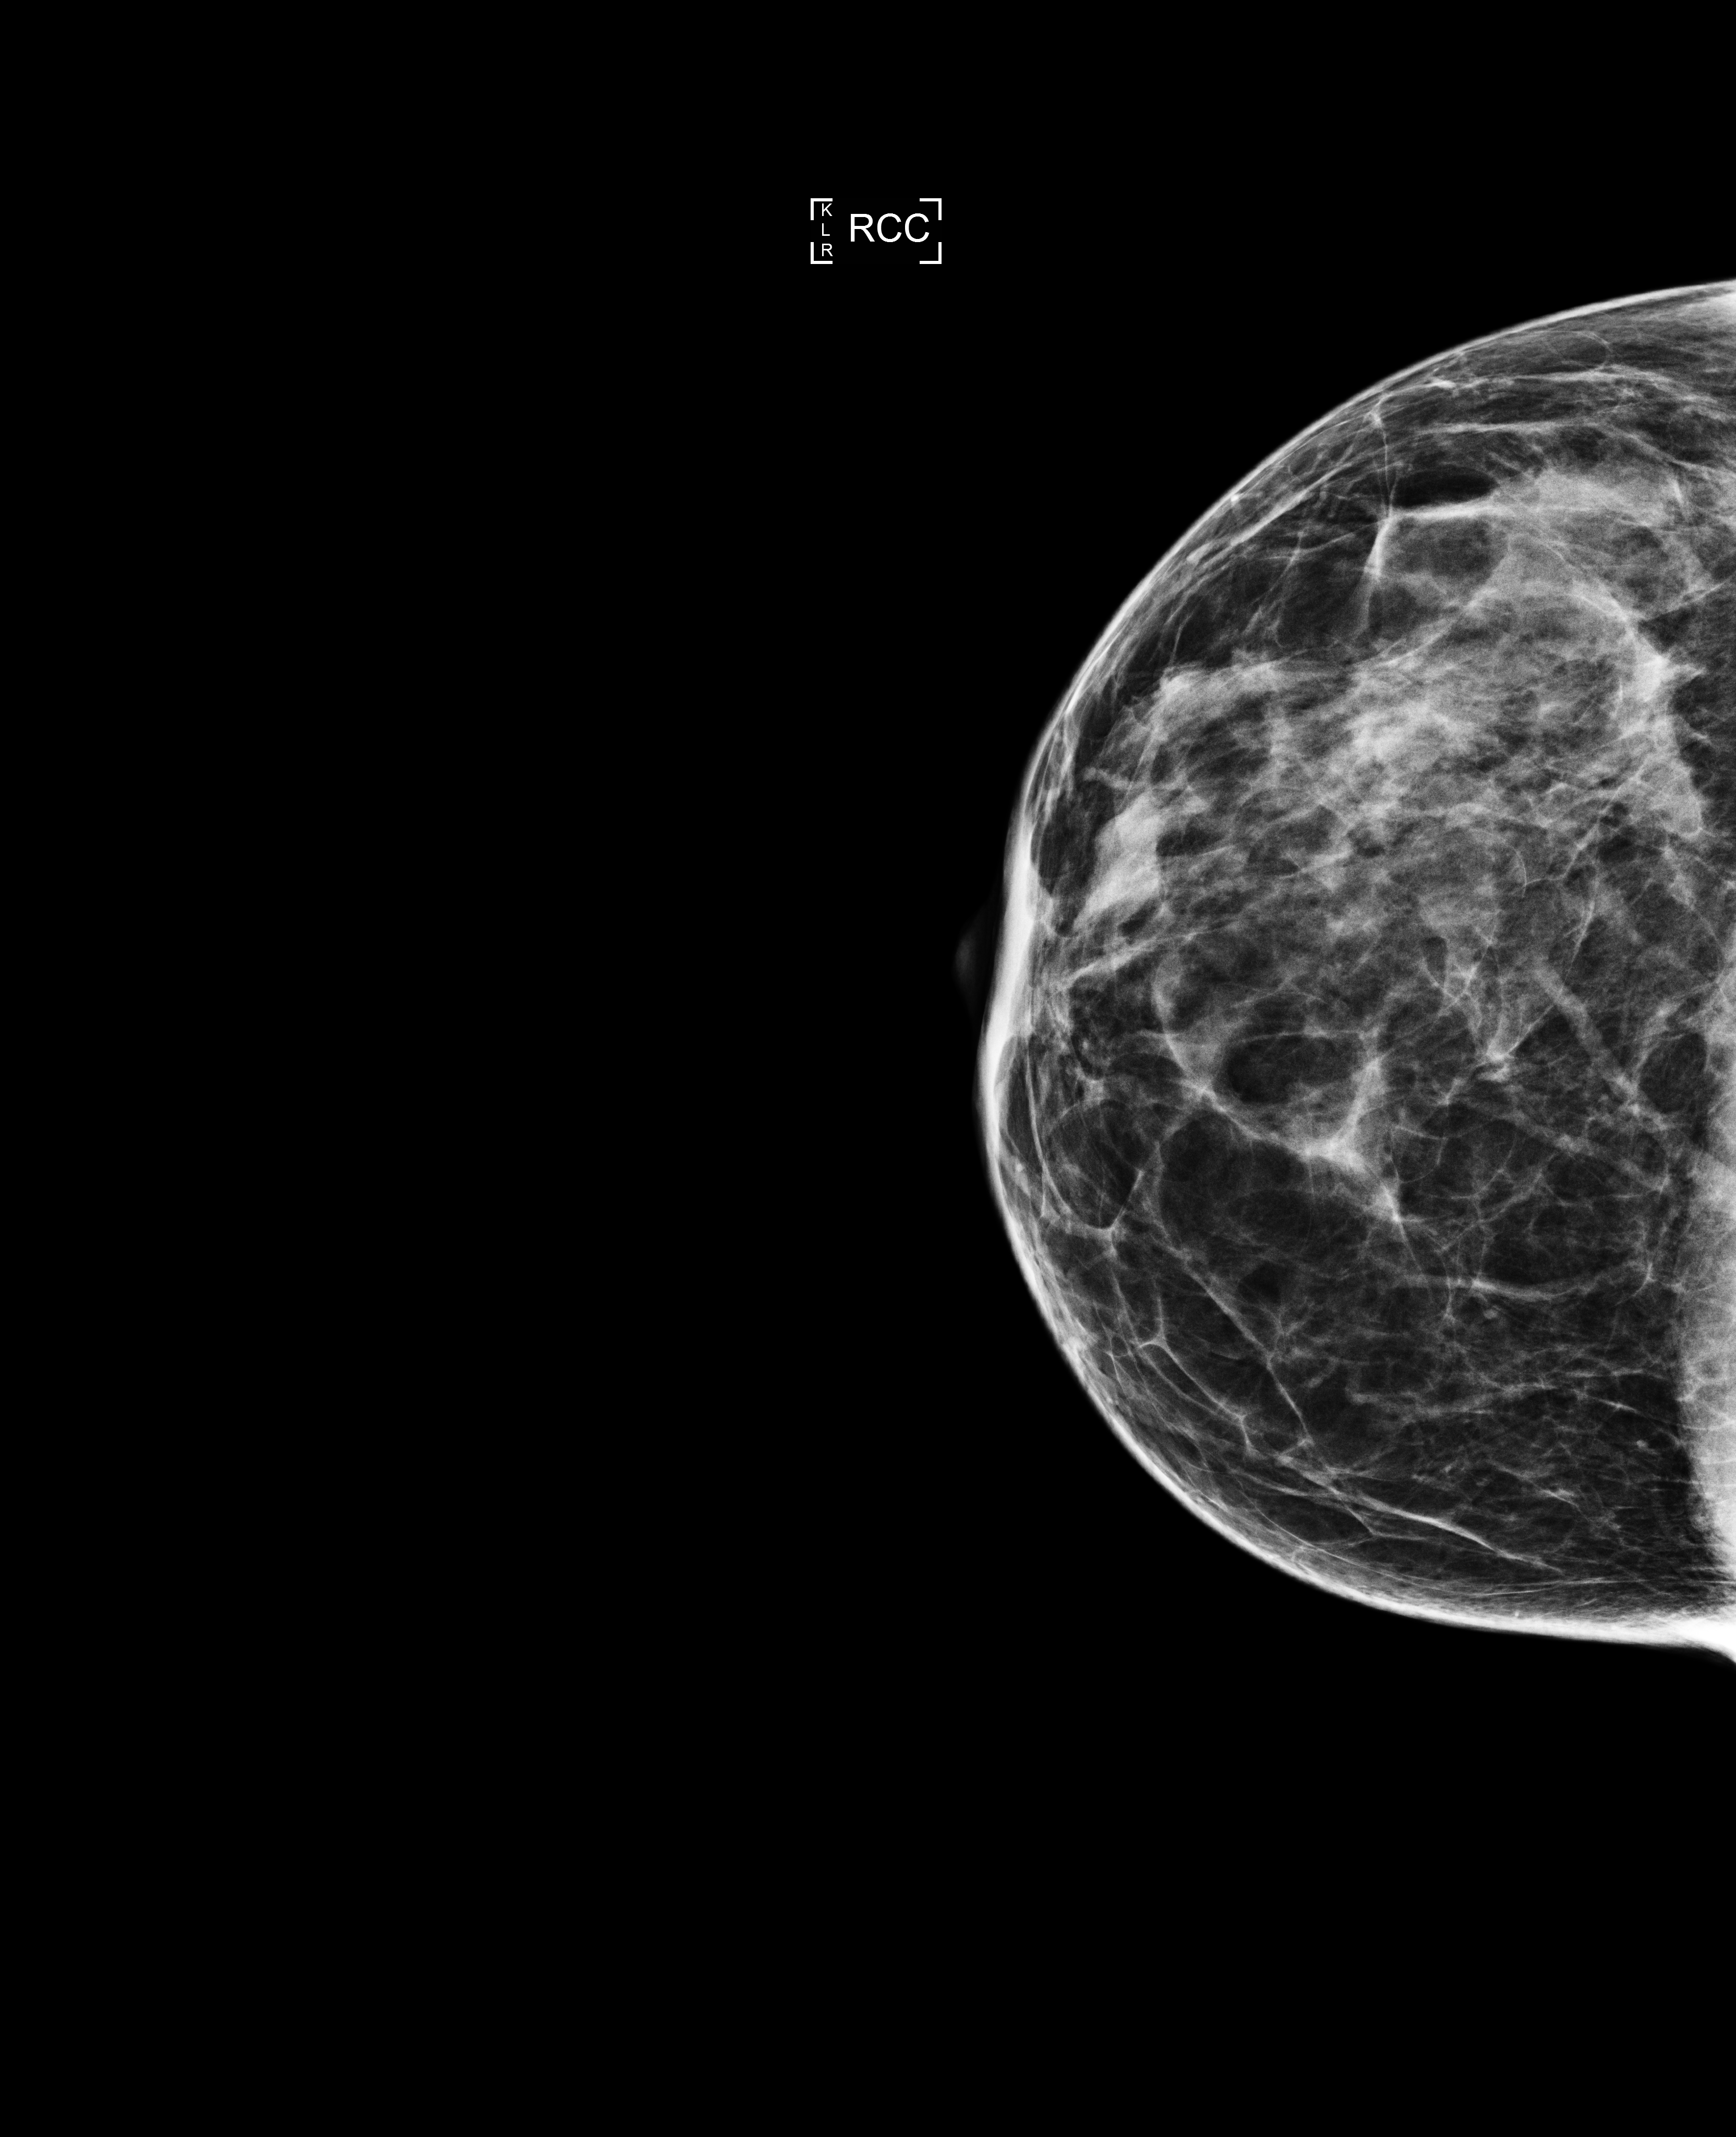
Annual screening mammography examination, compressed breast thickness 52 mm, system: Selenia Dimensions. Patient aged 41 years (female).
Image type: full-field digital mammogram. Breast: right. Projection: craniocaudal (CC) view.